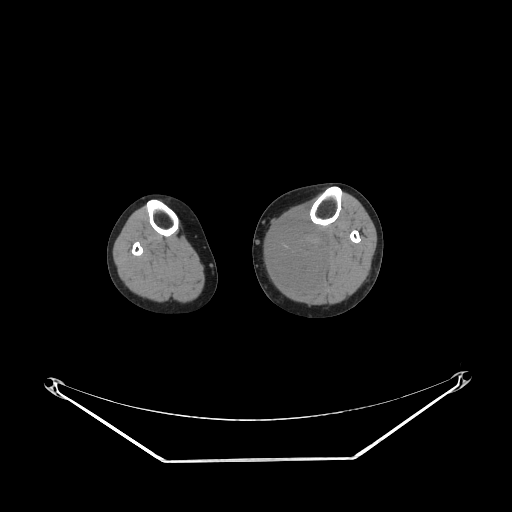
CT of an extremity soft-tissue mass (from a PET/CT study), one axial slice. Reconstruction kernel STANDARD. Soft-tissue window (W 400 / L 40 HU). 3.75 mm slice thickness. 512 × 512 image matrix. Female patient. Case-level facts recorded for this patient, not image findings: histological type: extraskeletal high grade osteogenic sarcoma; grade: high; site of the primary tumour: left calf.
Annotated regions visible in this slice (expert contour drawn on MRI and transferred to this co-registered scan by the dataset authors):
- gross tumour volume (mass): box from (x=270, y=221) to (x=328, y=286) px